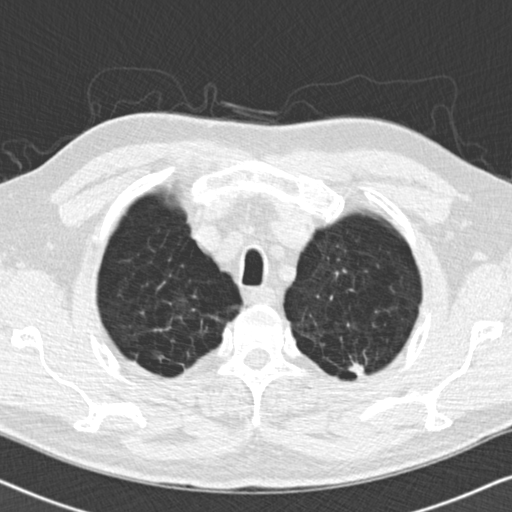
Low-dose screening chest CT, one axial slice; slice 154 of 175 in the series (ordered by position); reconstruction kernel B30f; 120 kVp; lung window (W 1500 / L -600 HU); 512 × 512 image matrix, field of view 330 × 330 mm.
Annotated regions visible in this slice (manually delineated by an expert):
- lesion 1 (tumor, upper lobe of left lung): bounding box (x1, y1, x2, y2) in pixels: (348, 361, 364, 376)